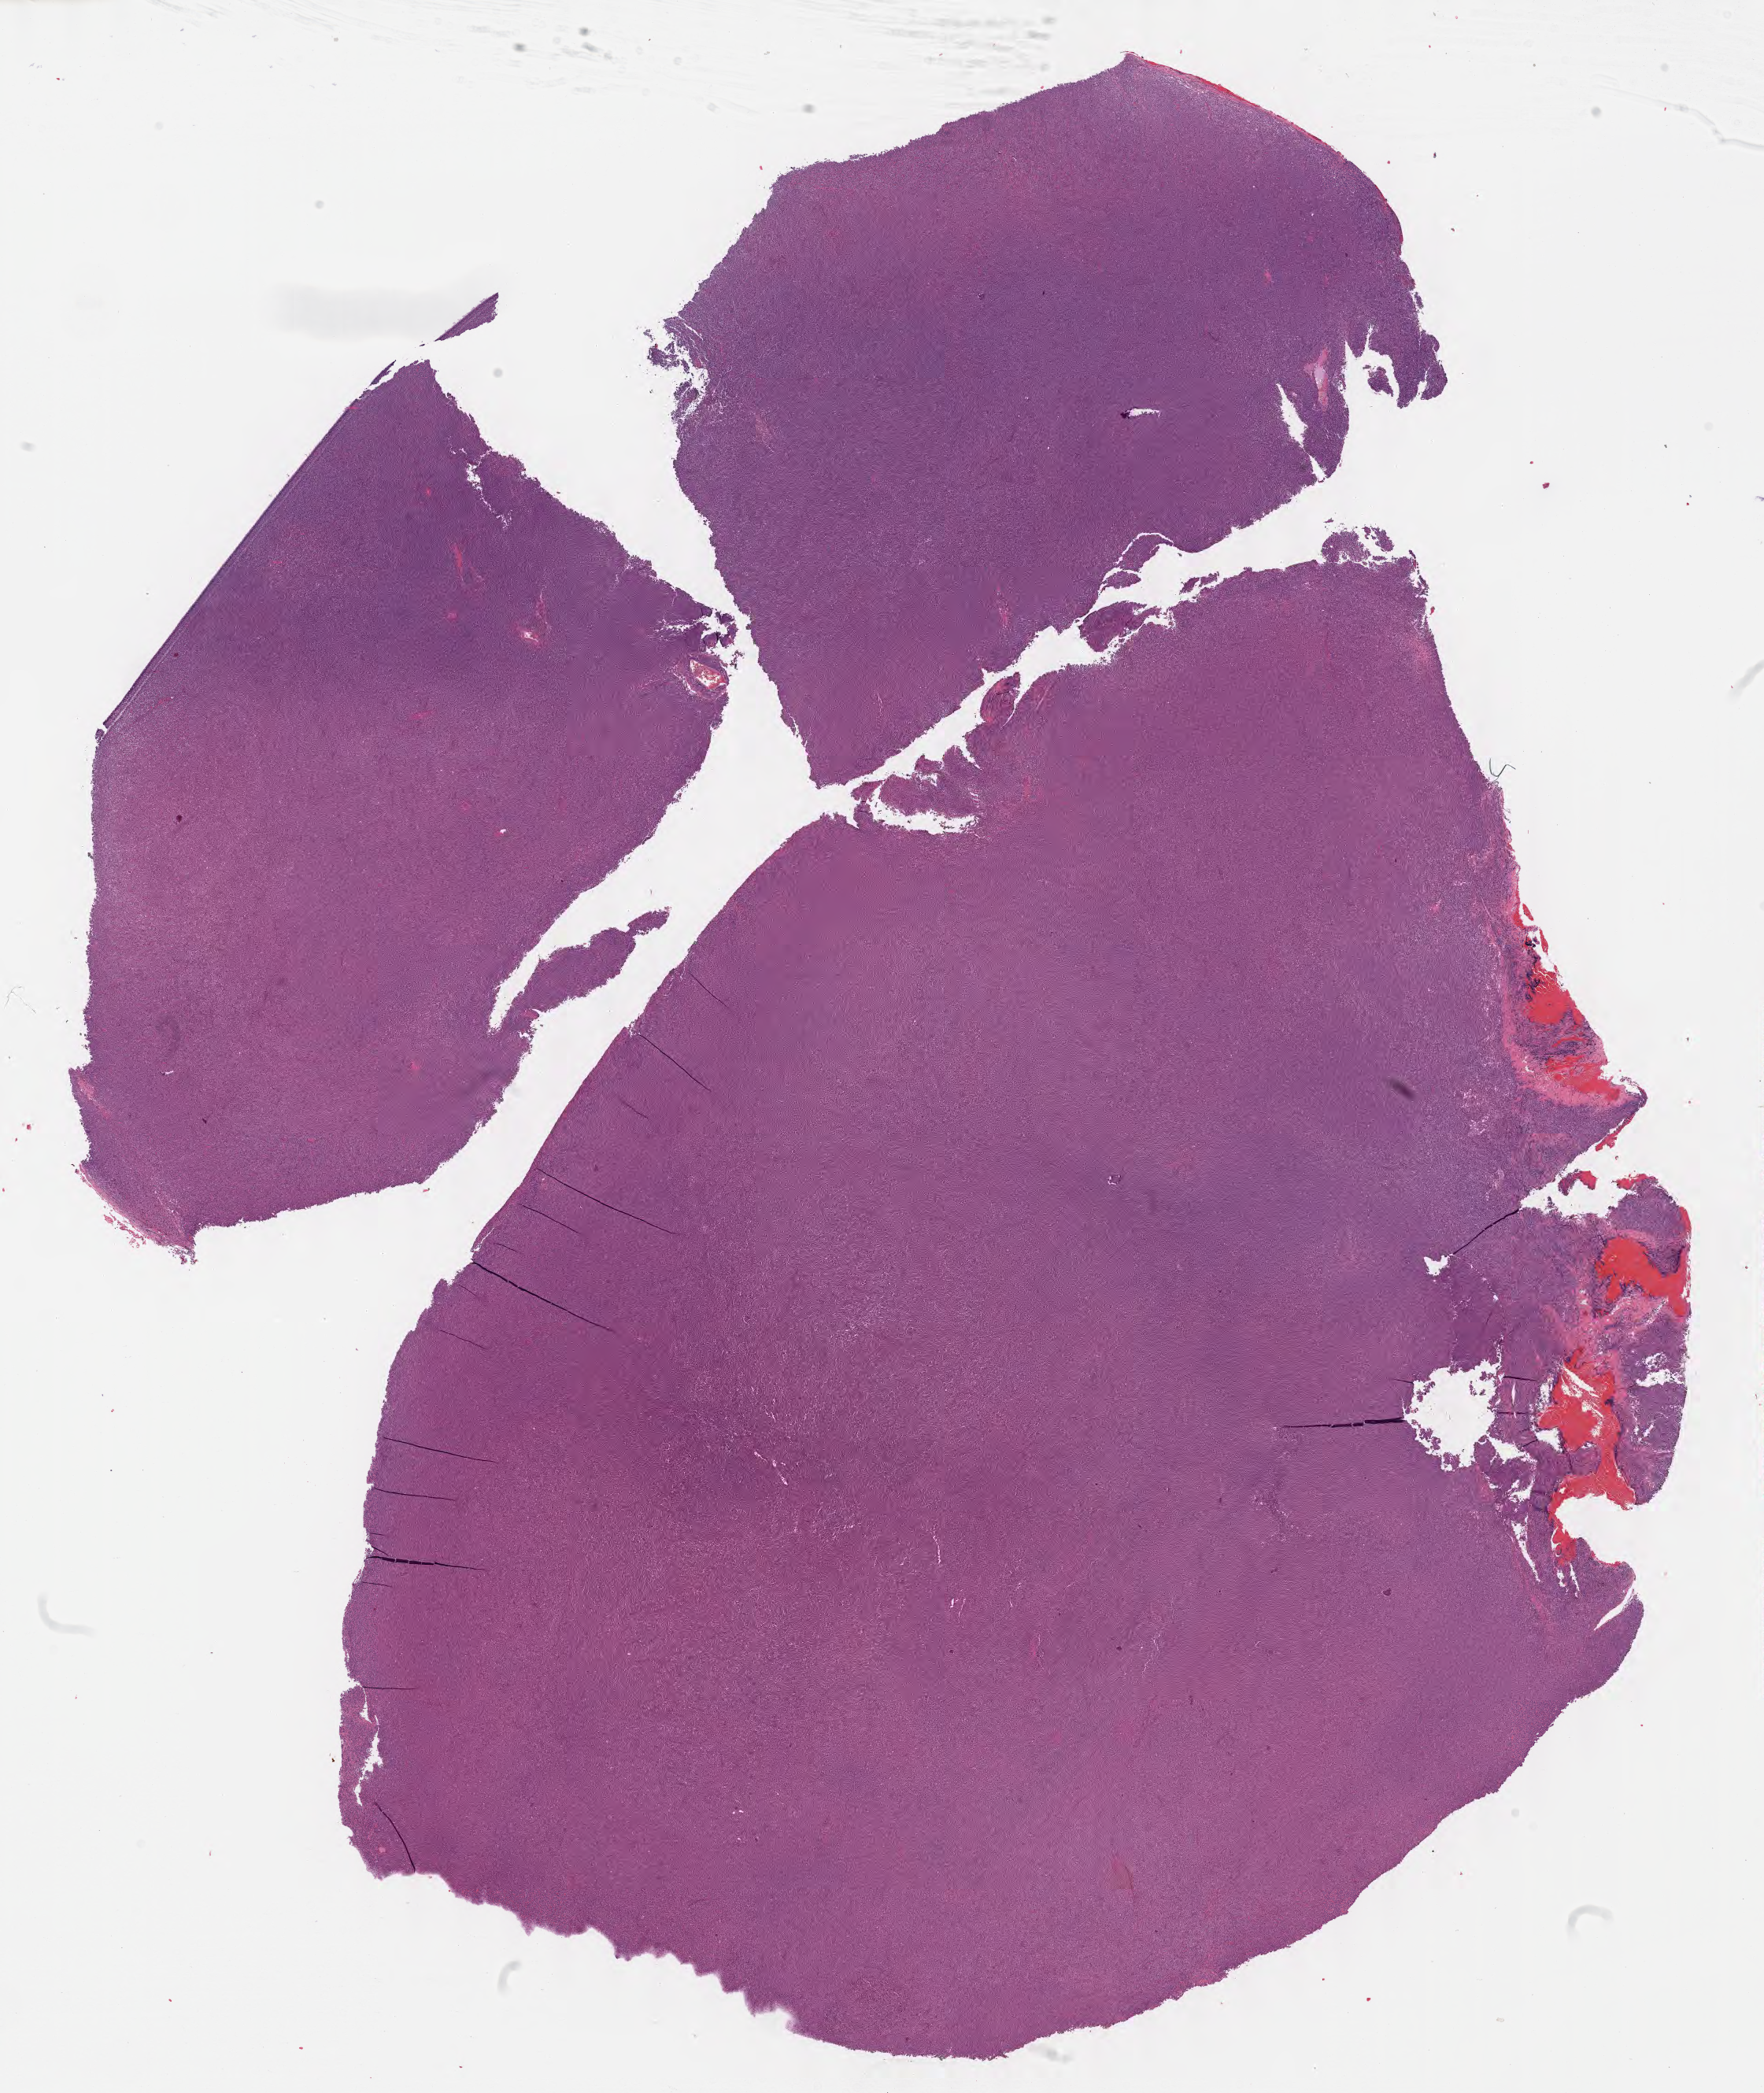
Digitized hematoxylin and eosin (H&E)-stained section, shown as a low-resolution overview of the whole scanned area (about 18.1 x 21.5 mm); tumor tissue; anatomic site: liver. Patient female; aged 46.
• histologic diagnosis: Diffuse large B-cell lymphoma, NOS